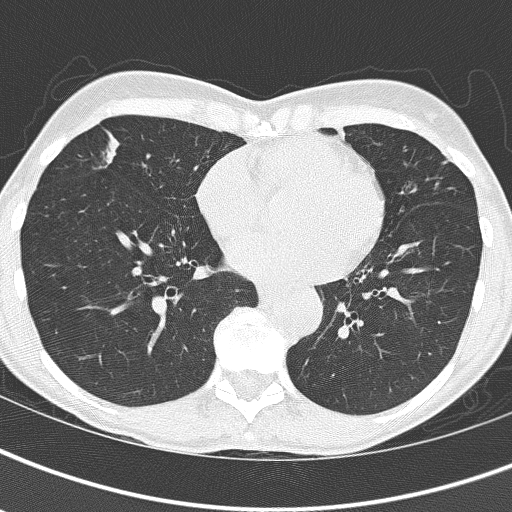
Chest CT (low-dose screening protocol), one axial image. First (baseline) screen. Lung window (W 1500 / L -600 HU). Lung (sharp) reconstruction kernel (B60f). Female participant, aged 67 years at enrolment.
- Expert reader's lesion annotation, bounding box <84,121,179,203> (left, top, right, bottom; pixels).
- Screening reader's record for this exam: no non-calcified nodule ≥4 mm recorded.
- Official screen result: negative screen, significant abnormalities not suspicious for lung cancer.
- Participant outcome: lung cancer diagnosed 832 days after this screen — bronchiolo-alveolar adenocarcinoma, NOS, right middle lobe, well differentiated (G1), stage IA (AJCC 6th edition), 25 mm at pathology.